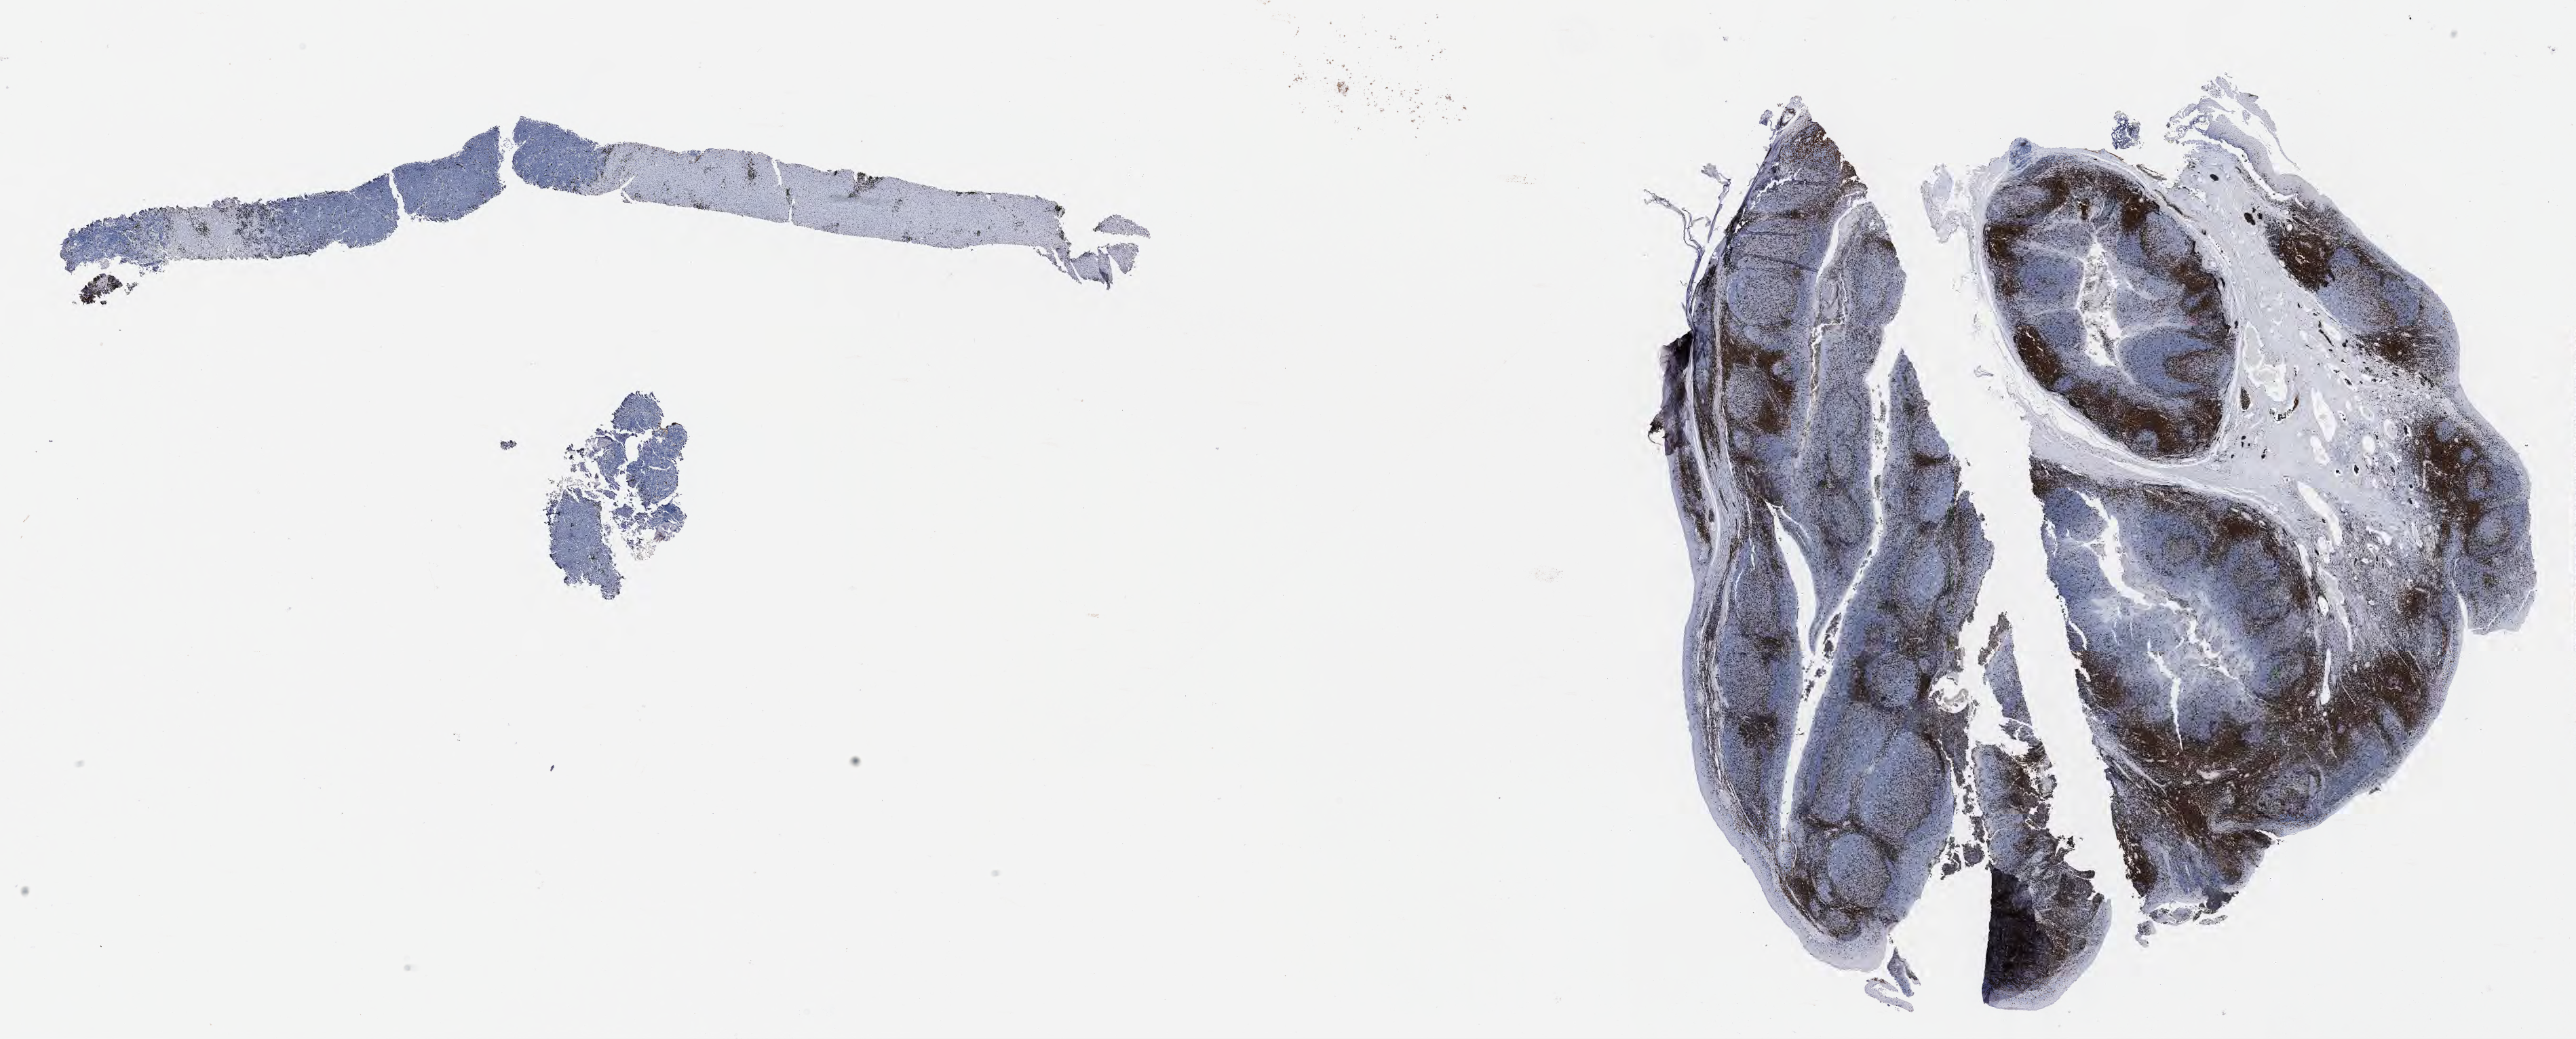
Whole-slide image, immunohistochemical stain for CD3, a low-resolution overview of the entire scanned area, about 30.7 x 12.4 mm, tumor tissue. Patient: male, 68 years old.
• diagnosis: Burkitt lymphoma, NOS